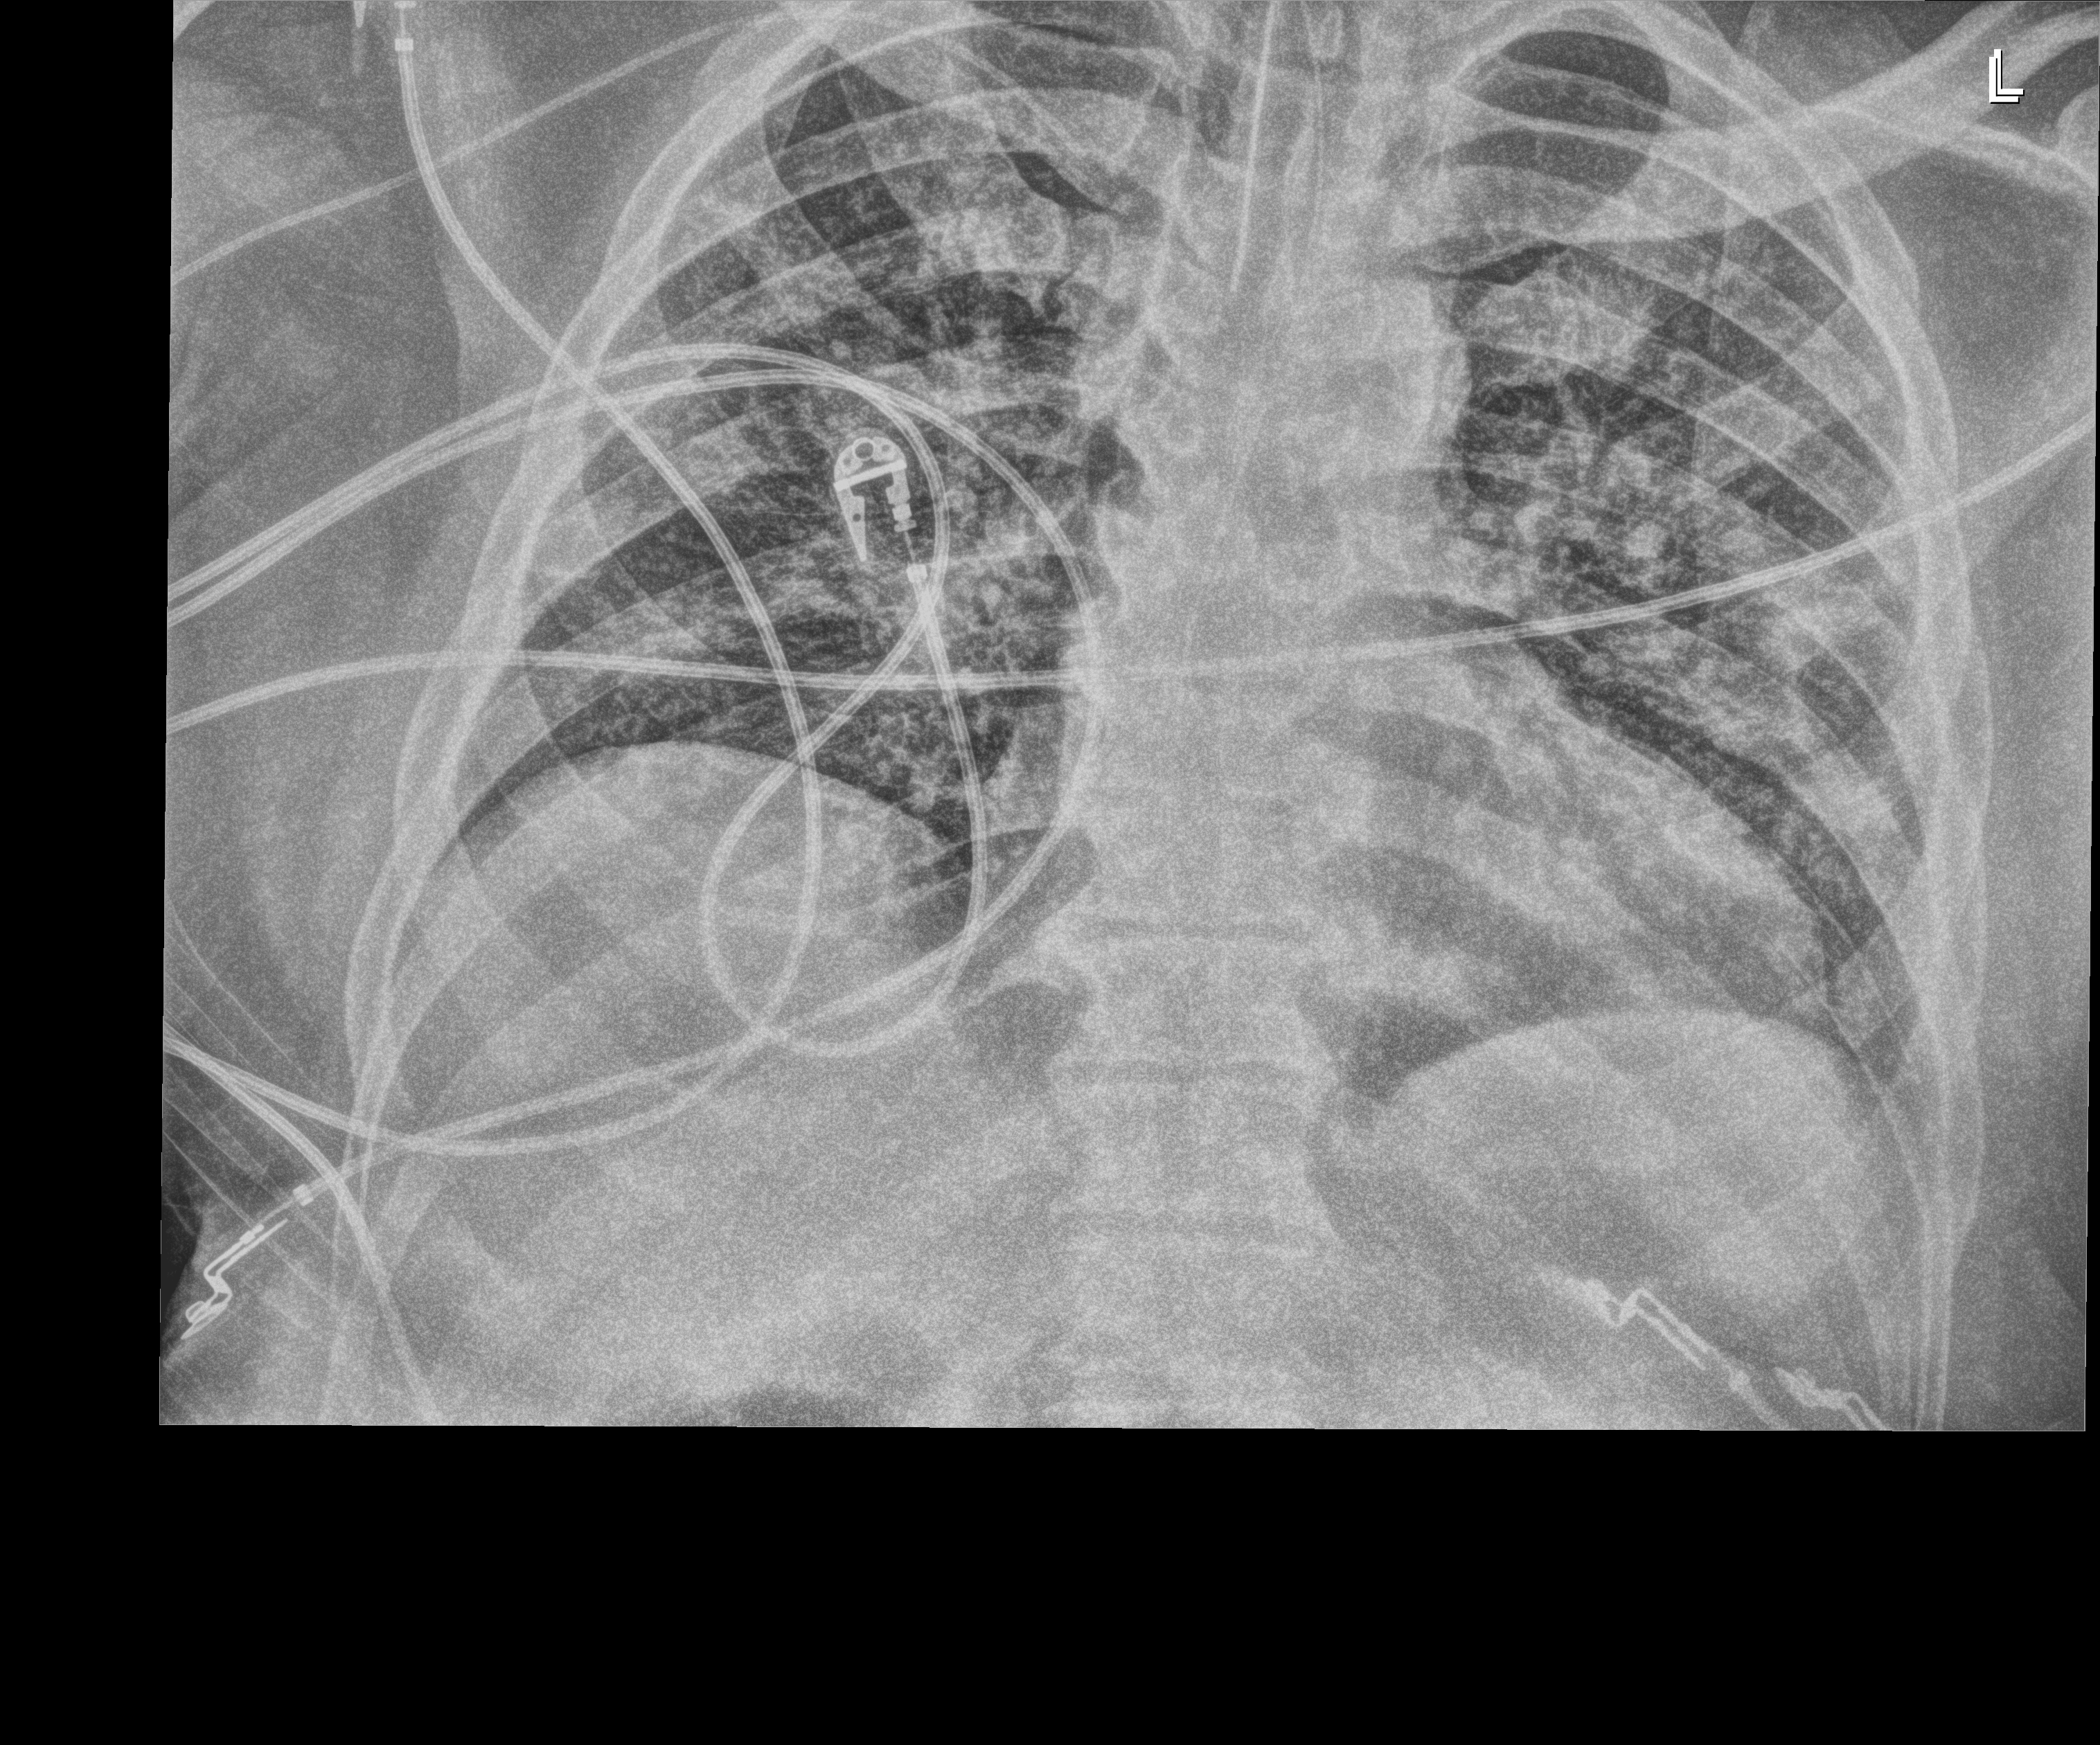
Chest X-ray; anteroposterior (AP) projection. Male patient hospitalised with COVID-19, age 18–59 years.
Admission-level facts for this patient (not findings on this image; timing relative to this image not recorded): chronic kidney disease (admission record): no; mechanically ventilated during this hospital stay: yes; smoking status (admission record): never.